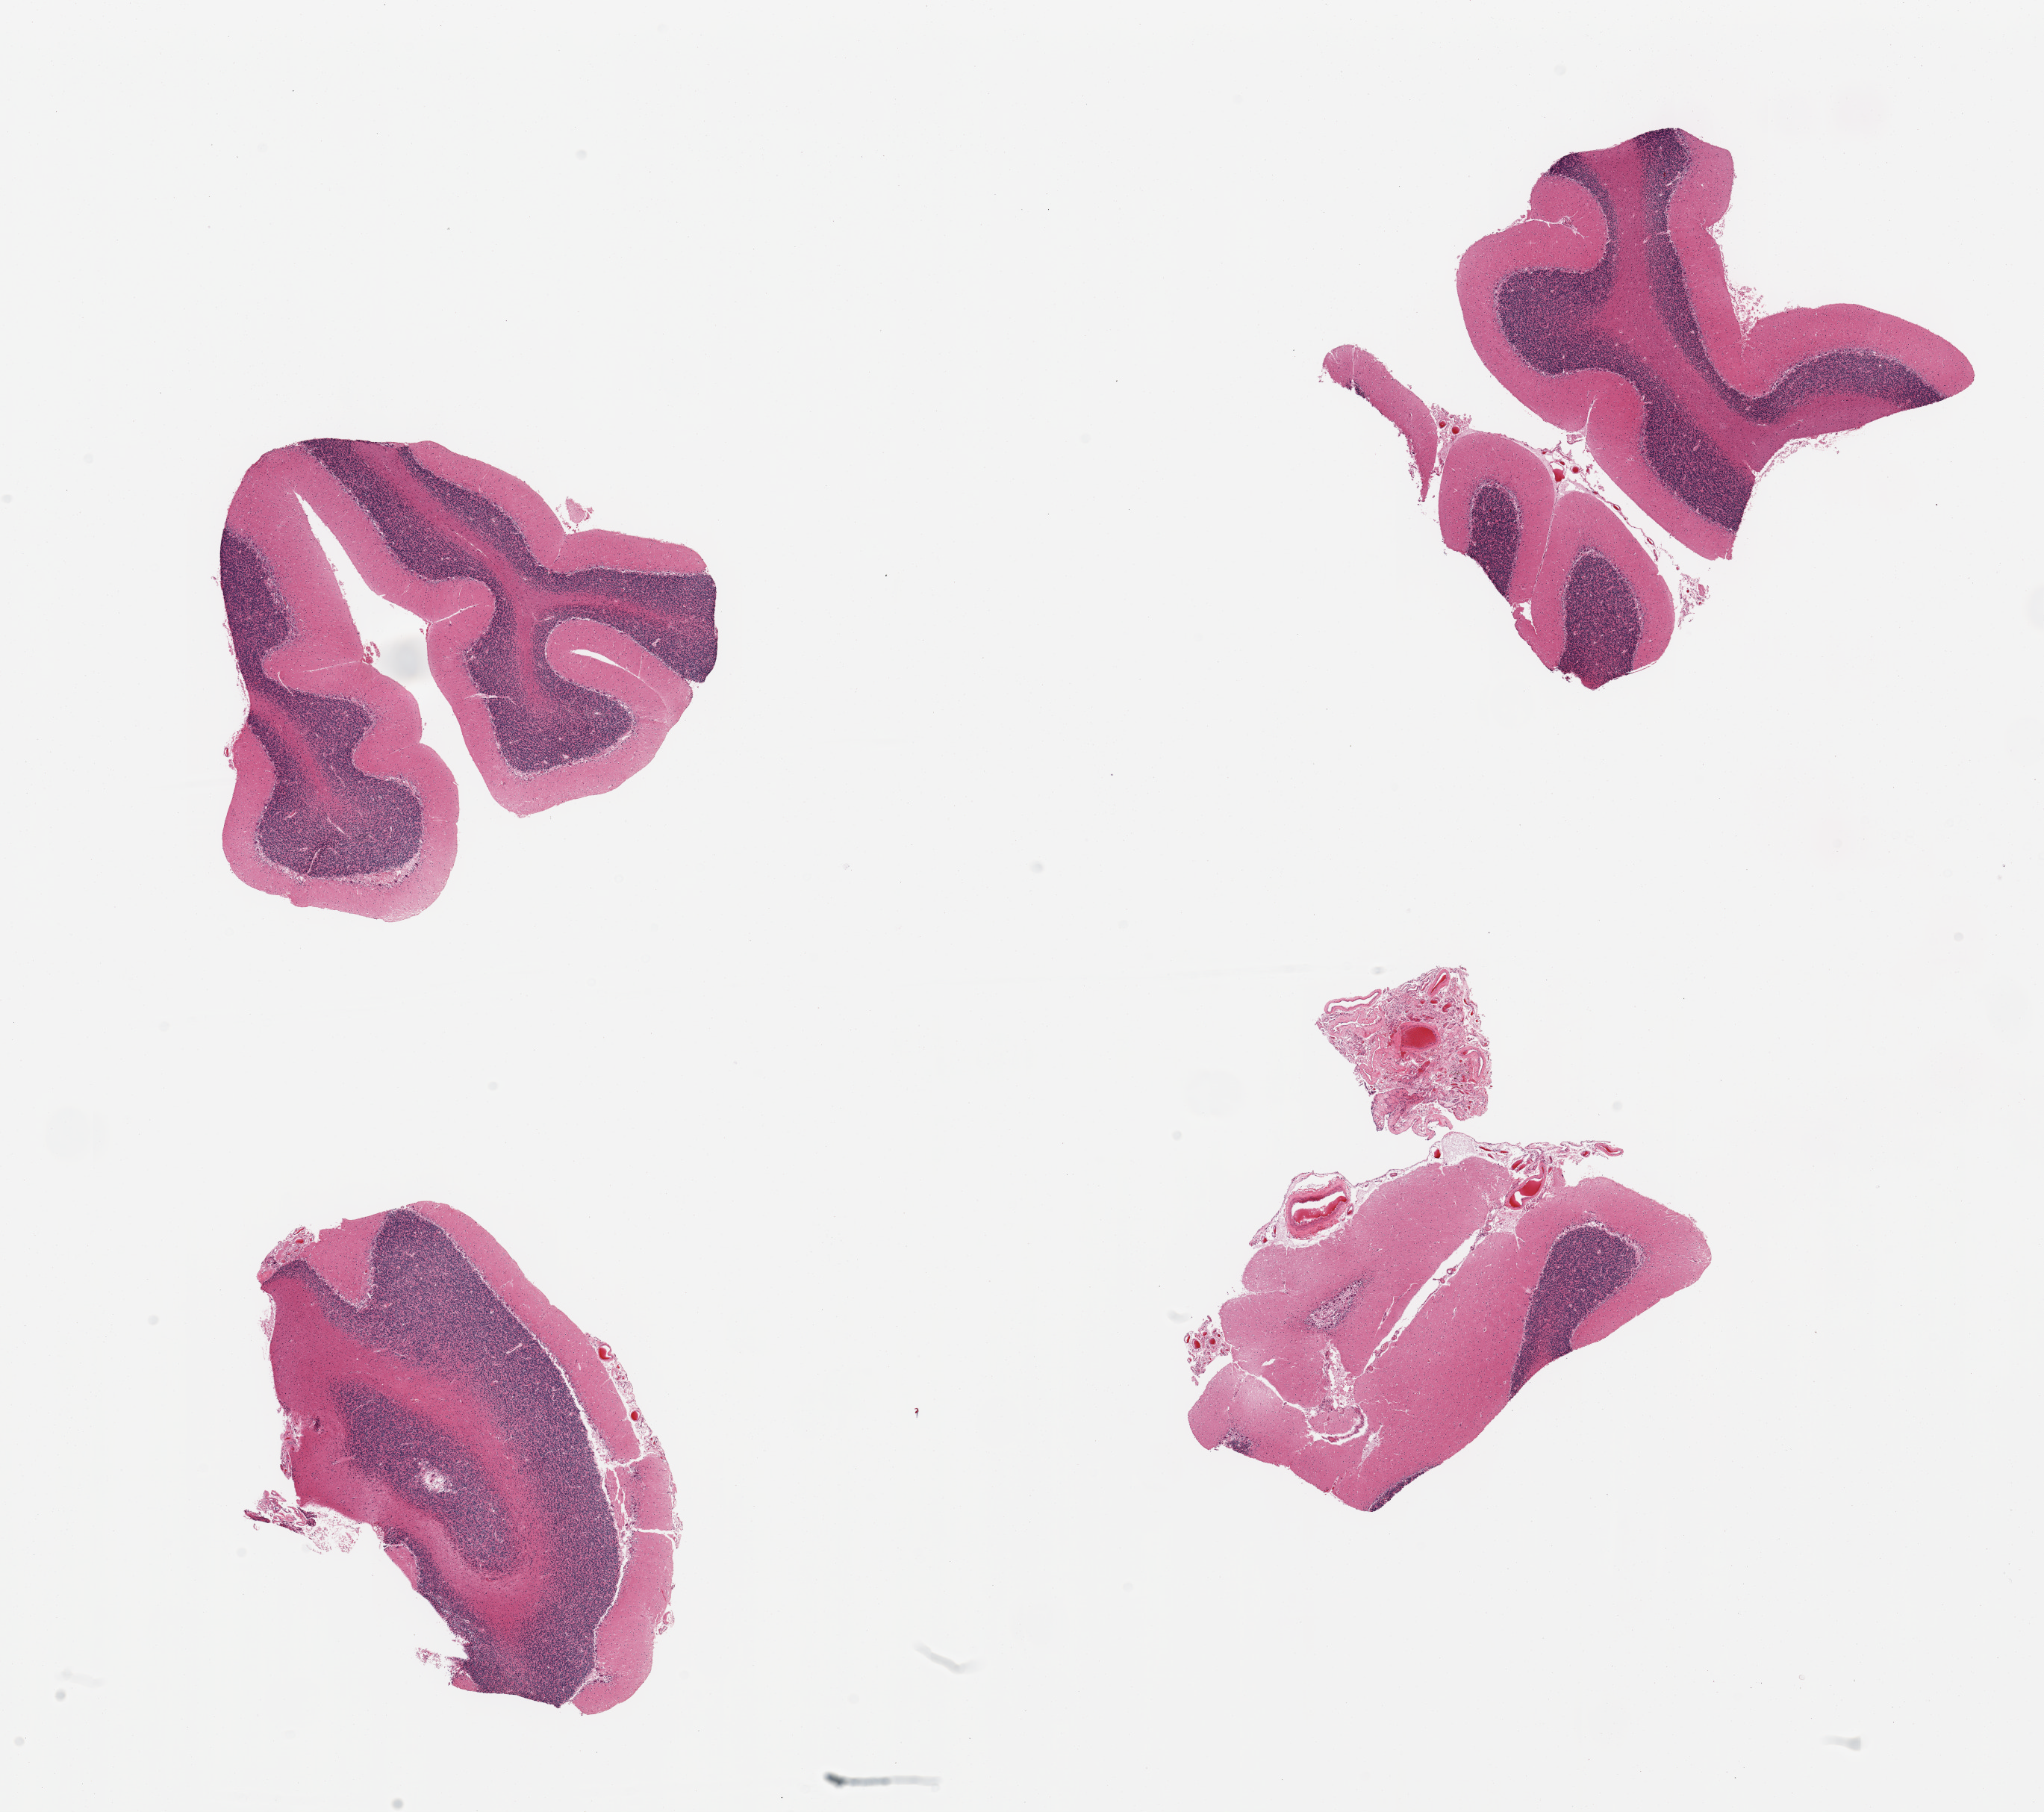
Digitized hematoxylin and eosin (H&E)-stained section, a low-resolution overview of the entire scanned area, about 21.7 x 19.2 mm (from a 20x scan); PAXgene-fixed paraffin-embedded (PFPE) section; sampled site (target tissue): cerebellum; donor tissue sample. Female donor.
Review note (as recorded): 4 pieces, no abnormalities.